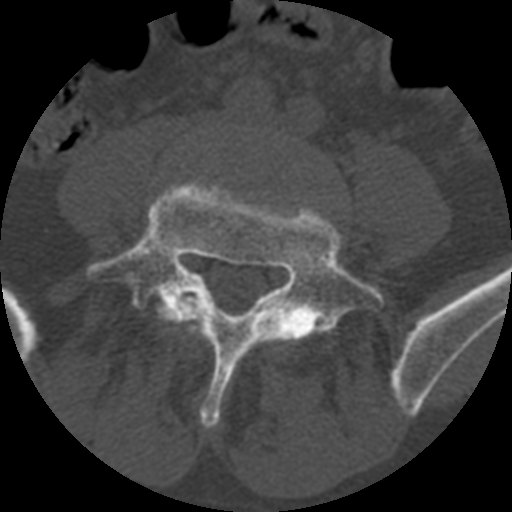
CT including the spine, one axial slice. Slice 261 of 399 in the series (ordered by position). Reconstruction kernel STANDARD. Bone window (W 1800 / L 400 HU). 1.25 mm slice thickness. 512 × 512 image matrix. Patient age 71 years. Case-level facts recorded for this patient, not image findings: primary cancer: prostate.
Outlined on this slice (semi-automatically segmented with operator editing):
- L4 vertebra: bounding box <174,295,197,324> (left, top, right, bottom; pixels)
- L5 vertebra: <85,179,384,427>